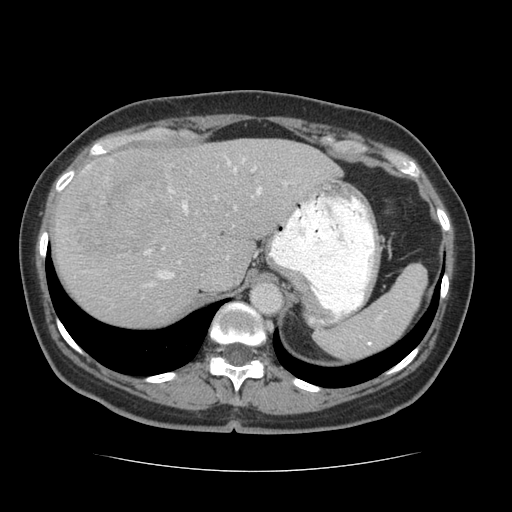
Contrast-enhanced abdominal CT (liver protocol), one axial slice; position 49 of 75 along the scan axis; 140 kVp; soft-tissue window (W 400 / L 40 HU); 2.5 mm slice thickness; 512 × 512 image matrix, field of view 360 × 360 mm. Case-level facts recorded for this patient, not image findings: diagnosis: hepatocellular carcinoma (patient treated with transarterial chemoembolisation; whether this scan precedes or follows treatment is not stated here); TNM stage (as recorded): Stage-I; Child-Pugh class: A; tumour nodularity: uninodular.
Outlined on this slice (semi-automatic segmentation, software-assisted and operator-edited):
- liver parenchyma outside the tumour (the mass and vessels are separate outlines, so this box may not span the whole liver): bounding box [x1, y1, x2, y2] px = [52, 138, 340, 326]
- mass: [60, 151, 177, 256]
- liver vessels: [86, 156, 315, 287]